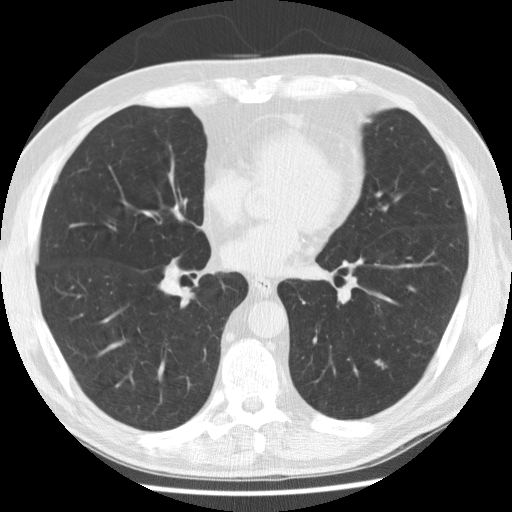
Axial slice from a low-dose chest CT screening exam; baseline screening round; lung window (W 1500 / L -600 HU); 2.5 mm slice thickness; standard (soft-tissue) reconstruction kernel (STANDARD); slice 148 of 265 in the series. Male, age 58 years at enrolment. Former smoker at enrolment.
- Expert reader's lesion annotation, bounding box [x1, y1, x2, y2] px = [367, 350, 401, 382].
- Screening reader's record for this exam: no non-calcified nodule ≥4 mm recorded.
- Official screen result: negative screen, no significant abnormalities.
- Later outcome: lung cancer diagnosed 798 days after this screen — adenocarcinoma, NOS, left lower lobe, poorly differentiated (G3), stage IA (AJCC 6th edition), 8 mm at pathology.